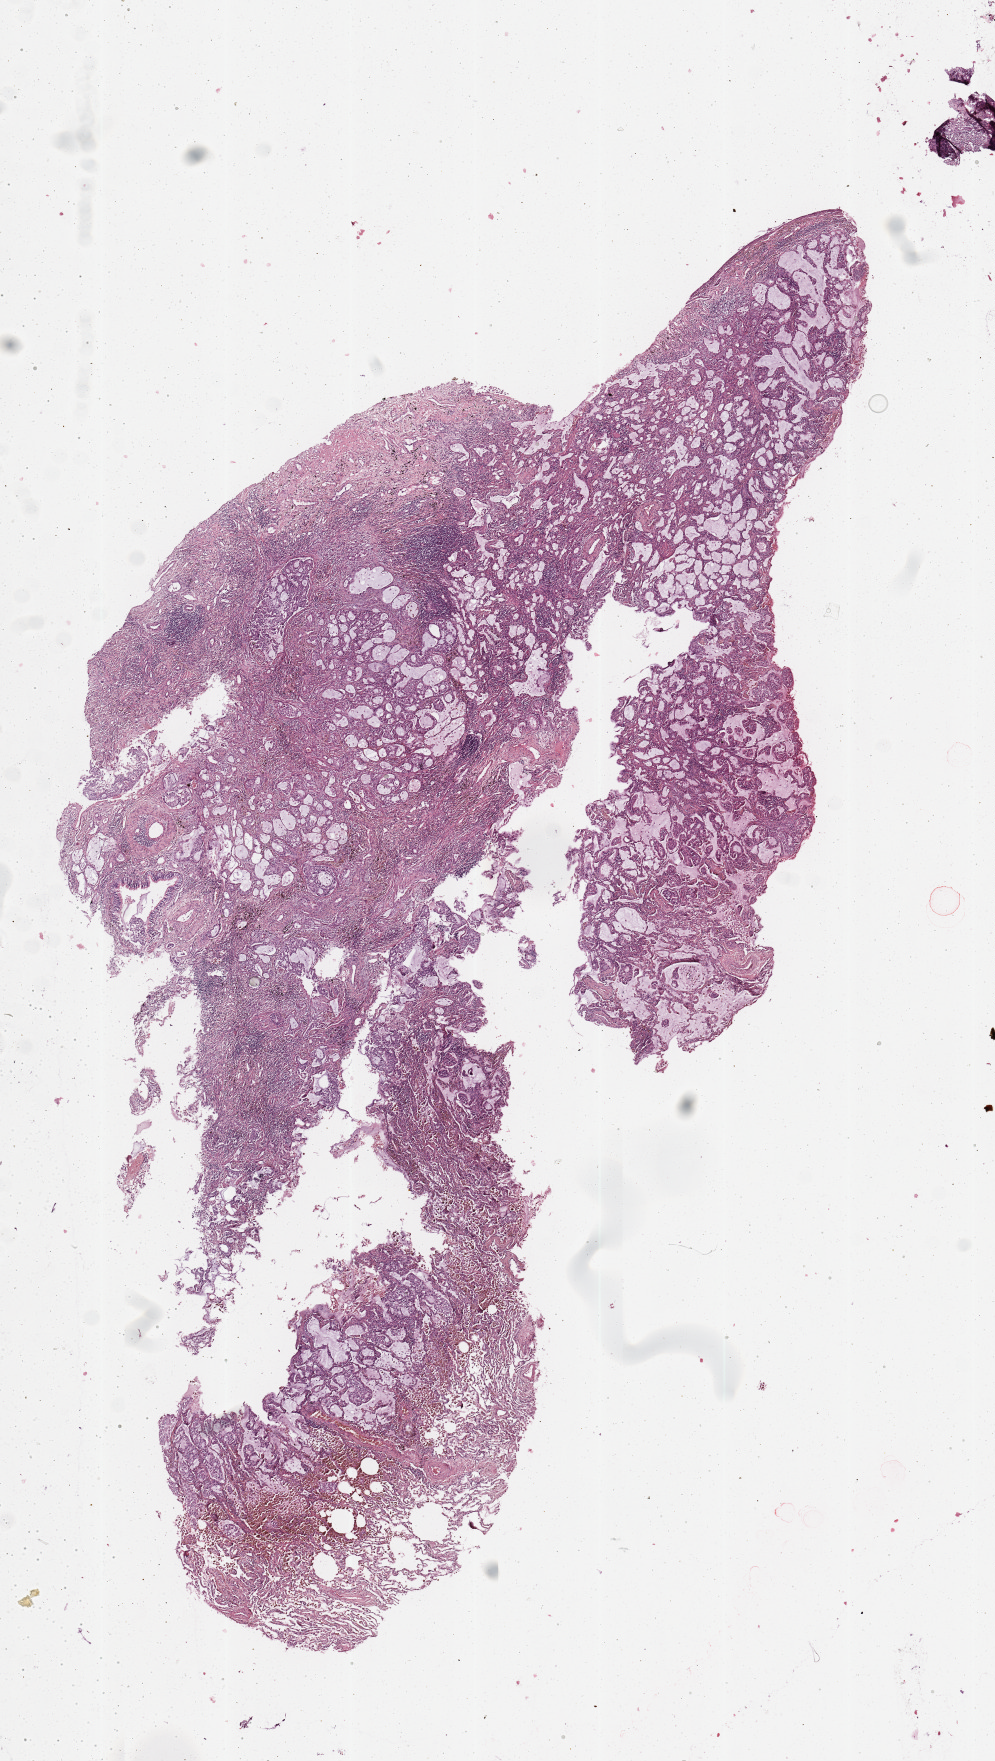
Whole-slide histology image, Hematoxylin and eosin (H&E) stained, a low-resolution overview of the entire scanned area, about 7.9 x 13.9 mm (from a 20x scan), tumour tissue sample, sampled site: lung. Male, 47 y/o. Histologic grade: G2 (moderately differentiated). Pathologist review of this section (percent, as recorded): tumour nuclei 70%, necrosis 5%.
* AJCC pathologic stage: IIA
* primary tumour site (as recorded): right upper lobe
* diagnosis: Adenocarcinoma, NOS